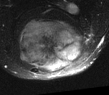
MRI of an extremity soft-tissue mass, one axial slice. Position 30 of 52 along the scan axis. T2-weighted fat-saturated. MR volume resampled by the dataset authors to the PET/CT grid (not the native acquisition matrix). 109 × 95 image matrix, field of view 106 × 93 mm. Male patient. Case-level facts recorded for this patient, not image findings: histological type: synovial sarcoma; site of the primary tumour: left poplietal fossa.
Annotated regions visible in this slice (expert contour drawn on MRI and transferred to this co-registered scan by the dataset authors):
- gross tumour volume (mass): box from (x=17, y=19) to (x=84, y=71) px